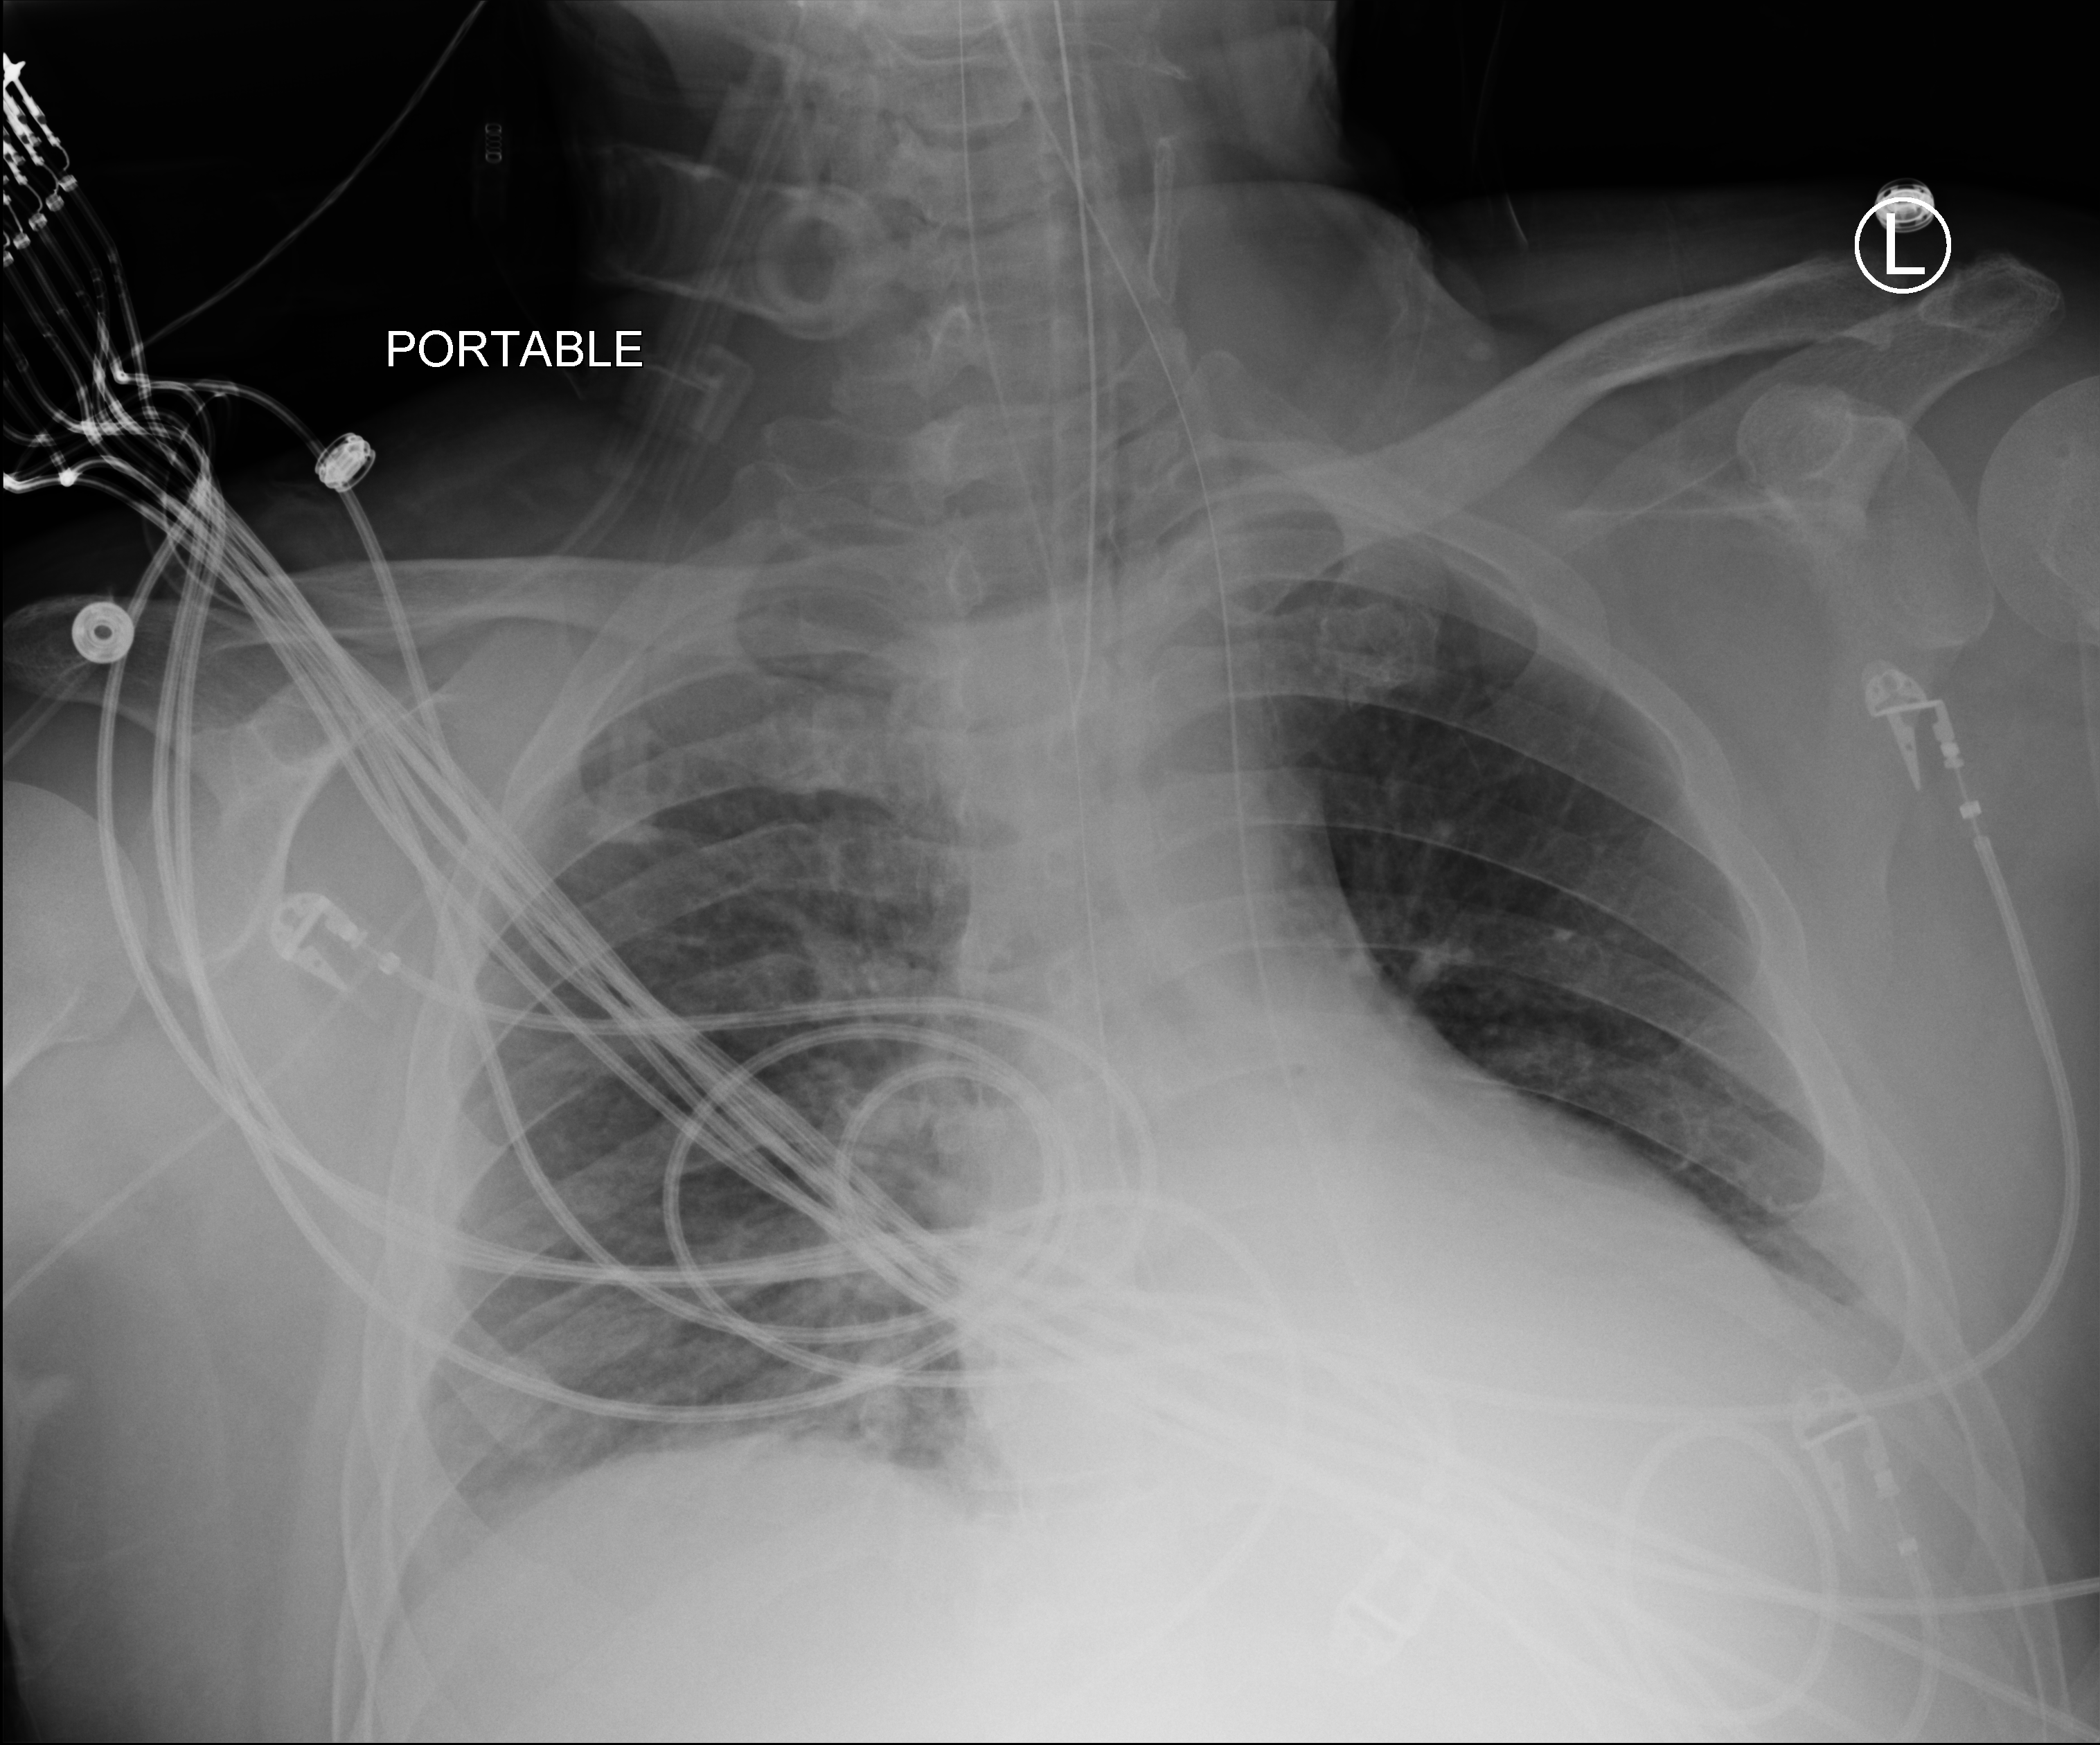
Chest X-ray (portable); anteroposterior (AP) projection. Patient hospitalised with COVID-19; male, aged 18–59 years.
From the hospital-stay record, not from the radiograph (when in the stay this image was taken is not recorded): admitted to intensive care during this hospital stay: yes; mechanically ventilated during this hospital stay: yes.